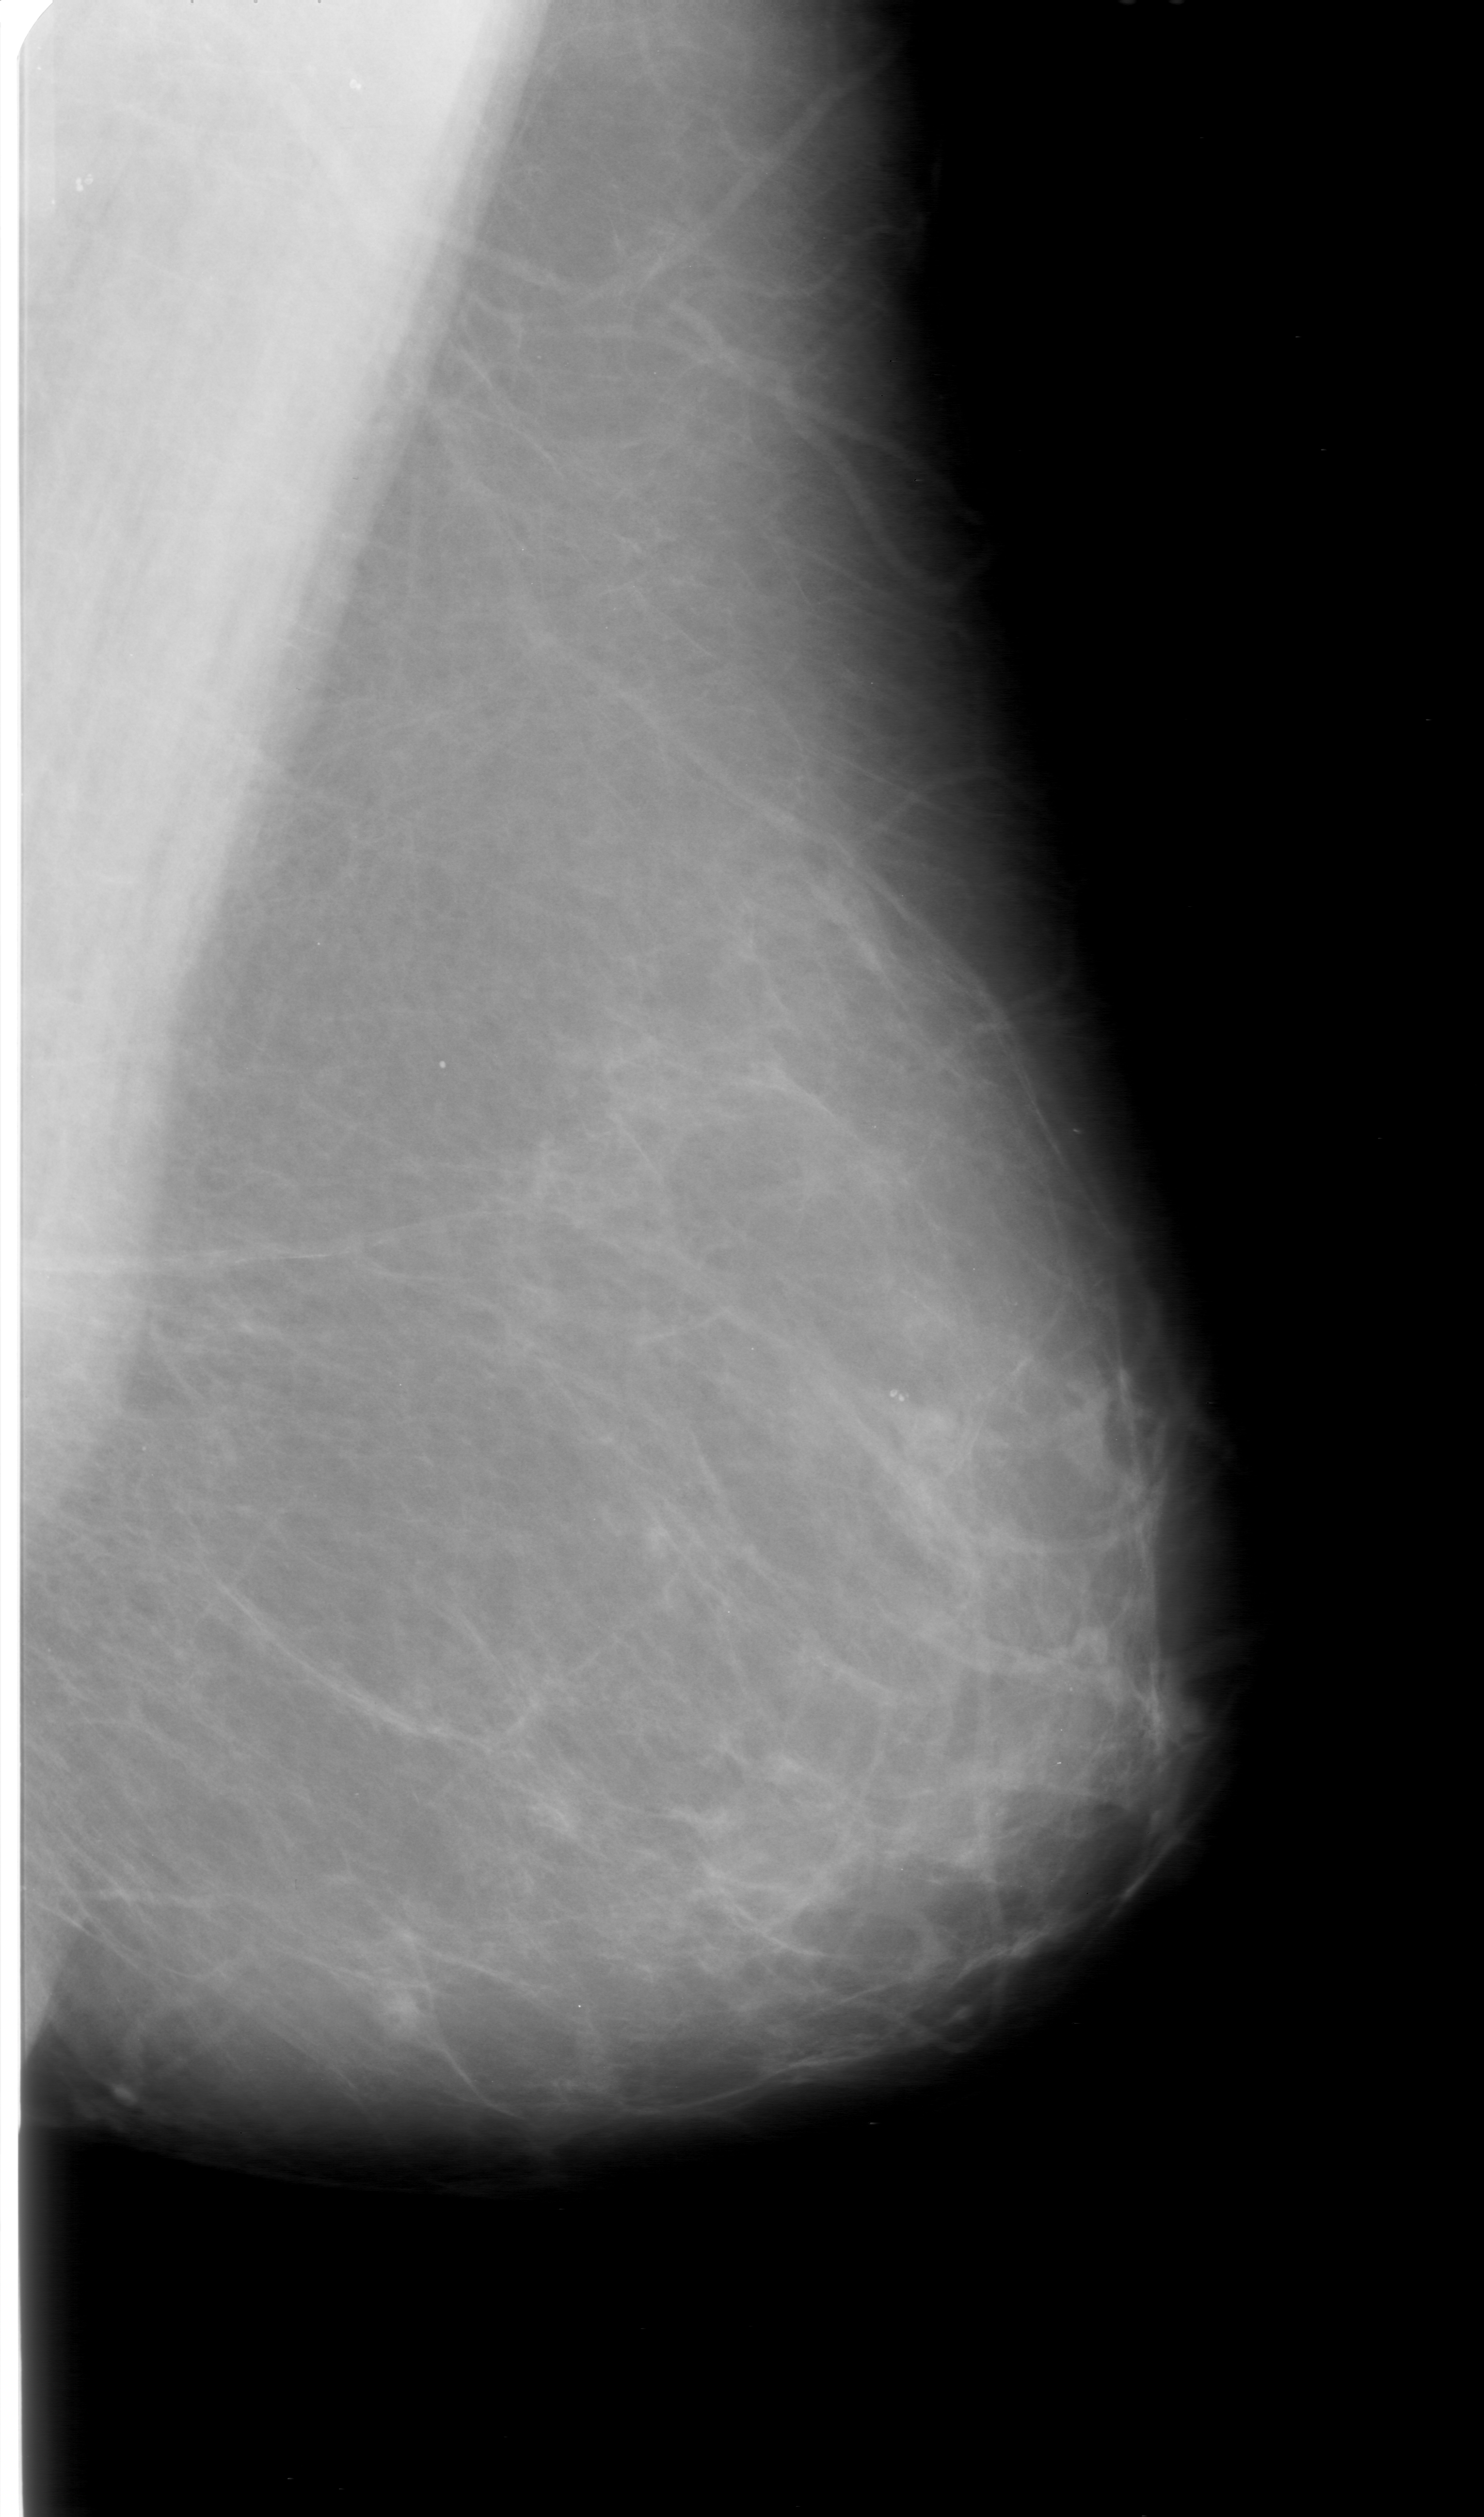
Mammogram (digitized film). Left breast. MLO view. 1484 × 2517 image matrix.
Marked abnormalities (boxes around the expert regions of interest):
- mass, shape lobulated, margins obscured; BI-RADS assessment category 0 (incomplete: needs additional imaging); pathology (as recorded): malignant: bounding box <365,1977,442,2059> (left, top, right, bottom; pixels)